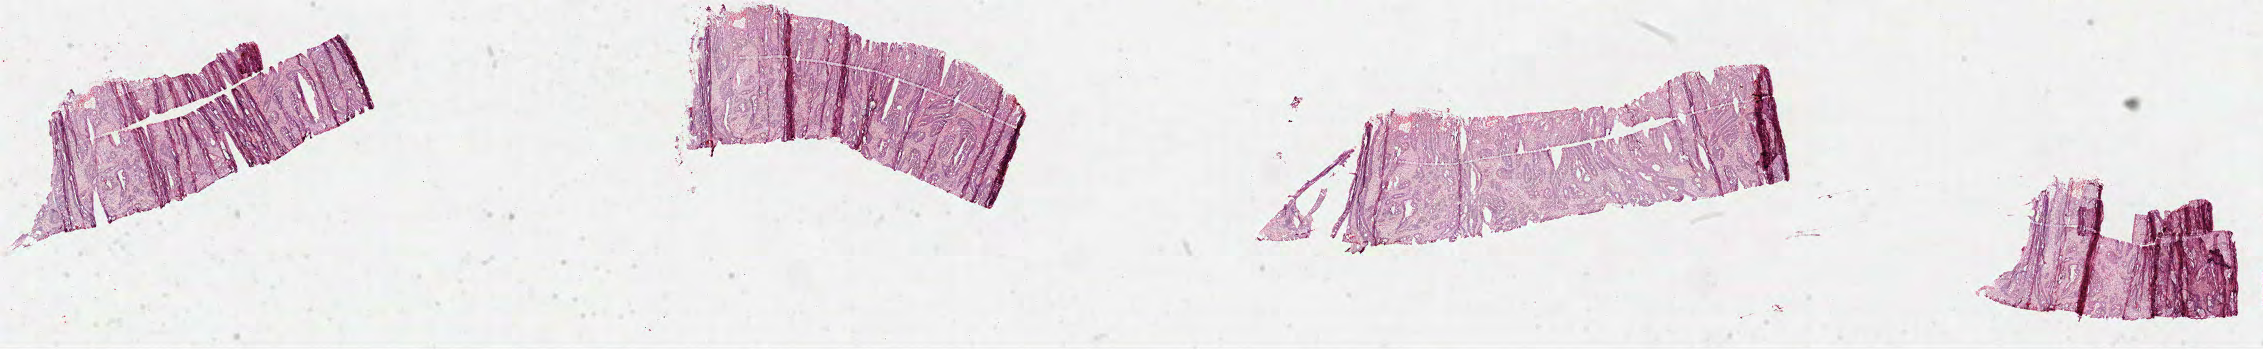
H&E-stained whole-slide image, whole scanned area (about 36.5 x 5.6 mm) shown as a low-resolution overview; FFPE section; primary tumour sample from the colon. Male patient; age at initial diagnosis 57 years.
Histologic diagnosis: Adenocarcinoma, NOS (sigmoid colon). AJCC pathologic stage: I.